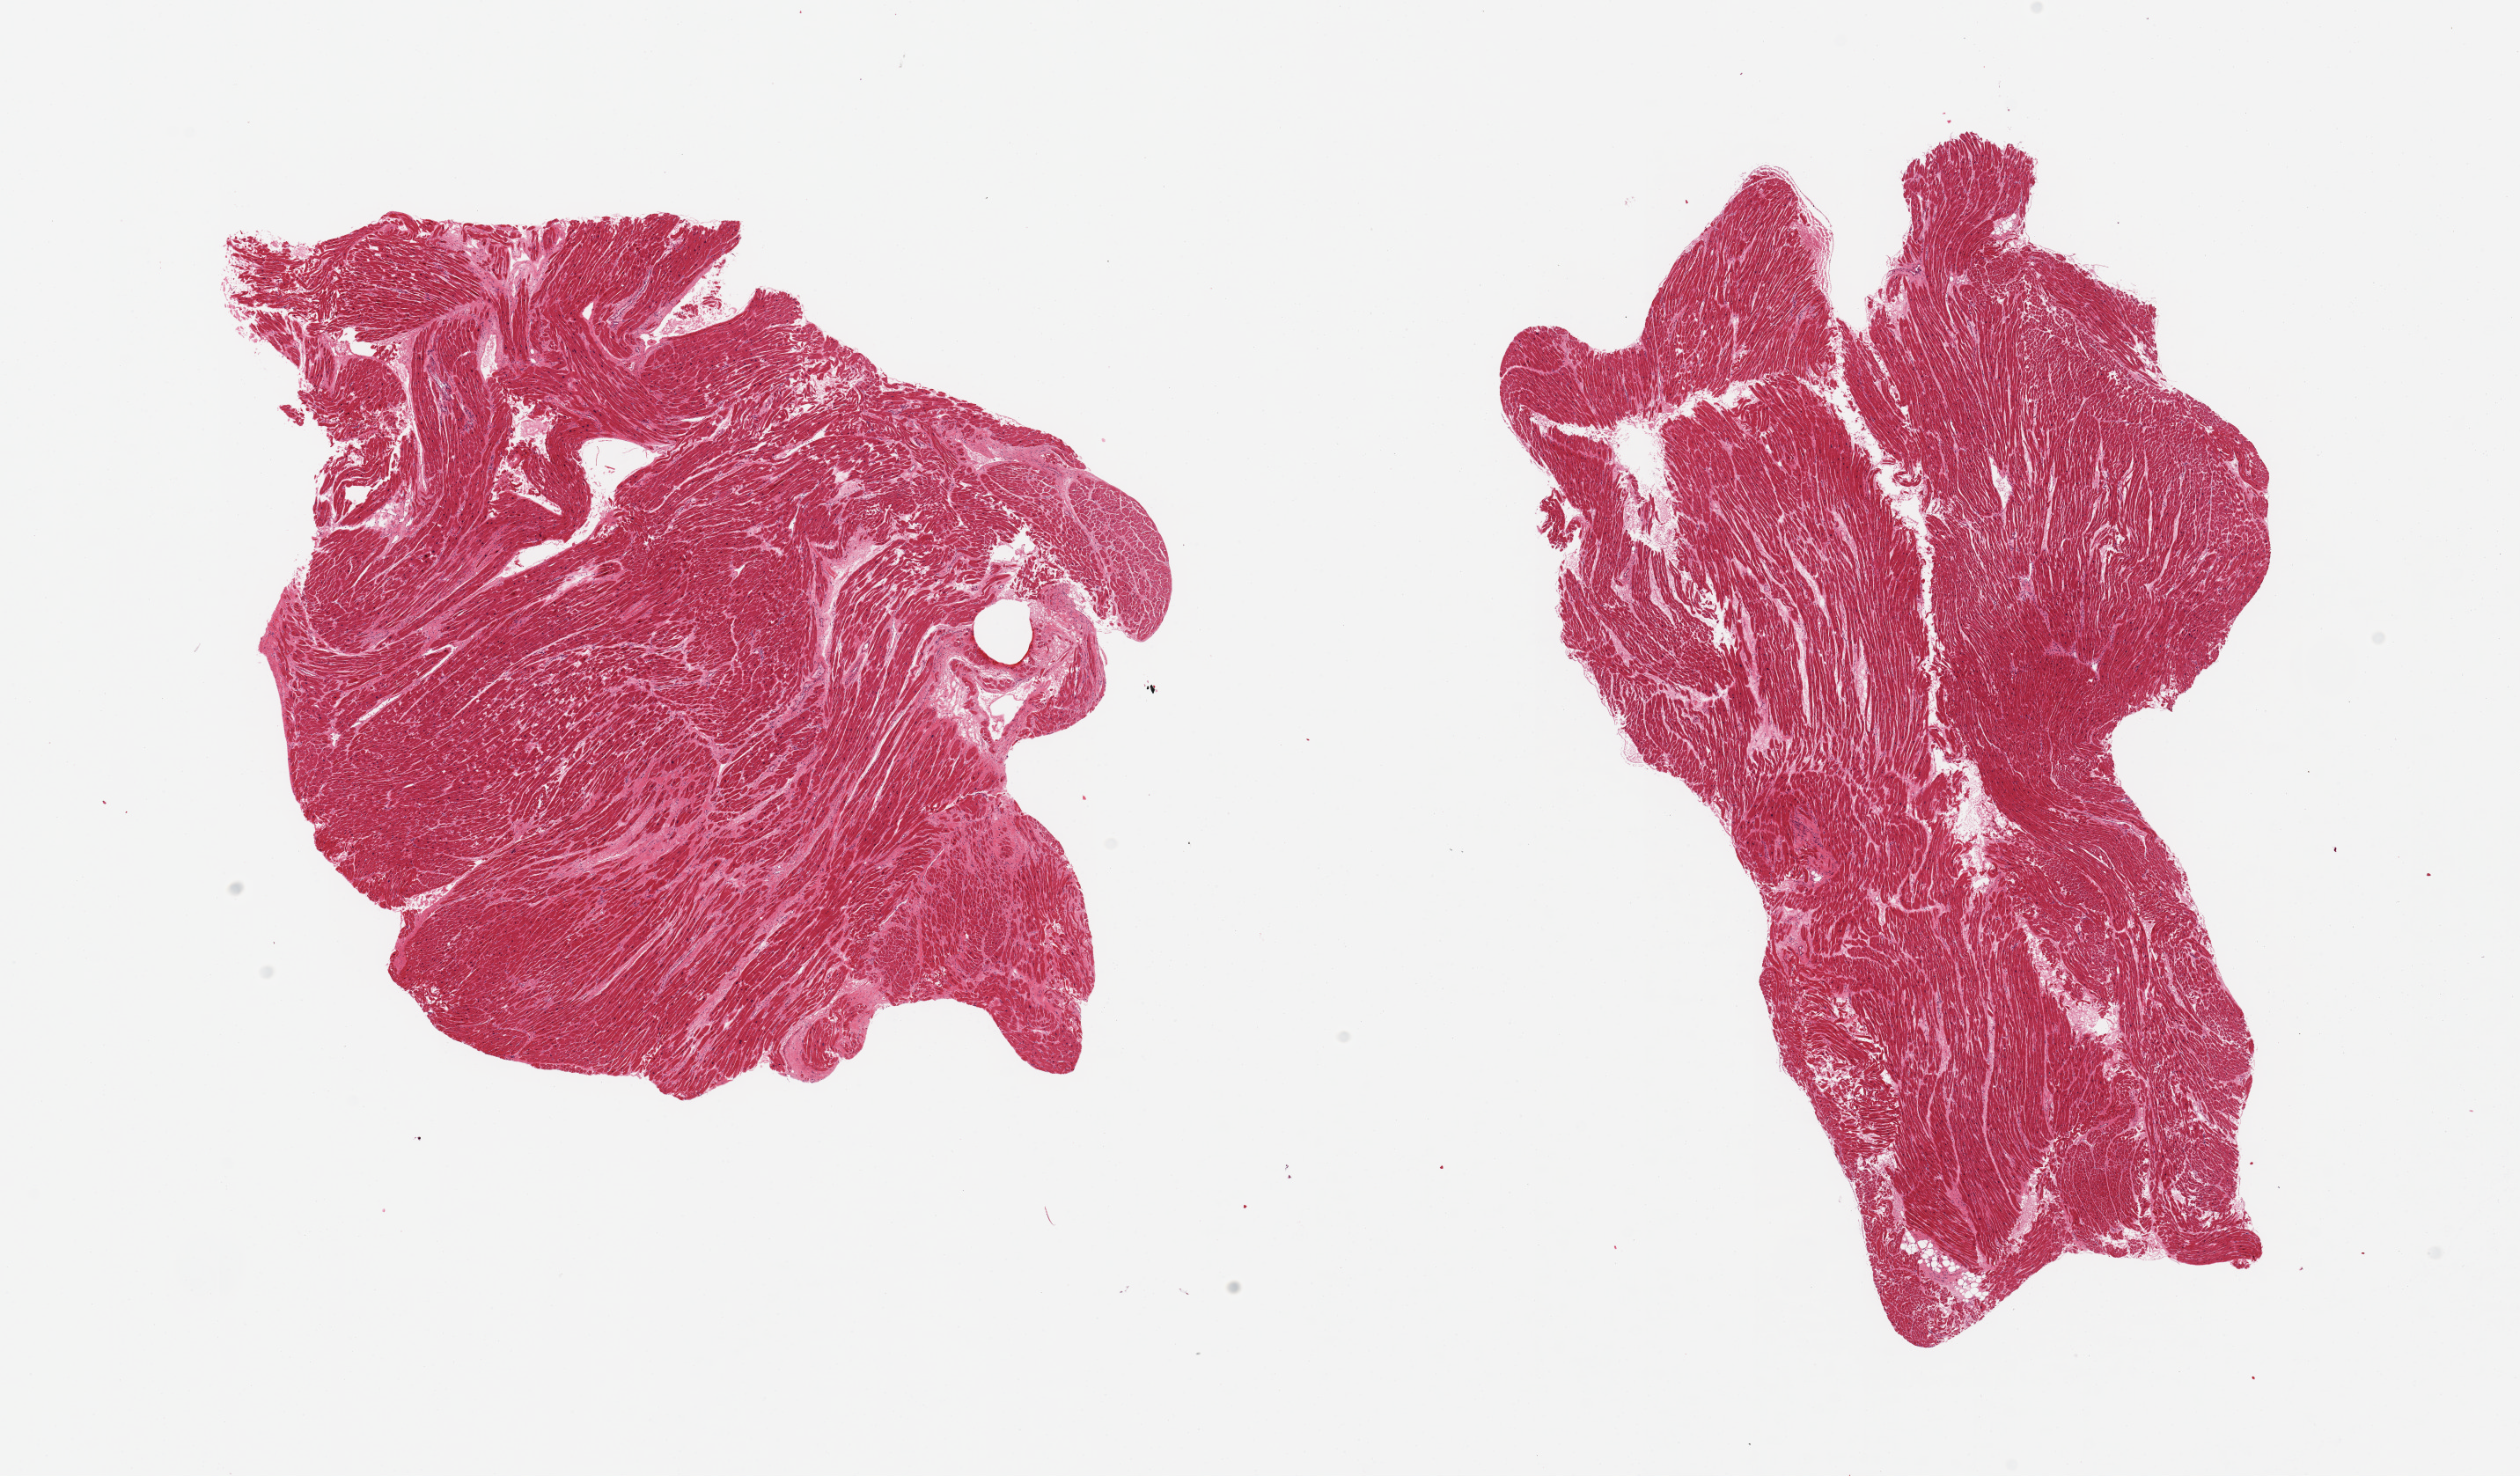
Haematoxylin and eosin whole-slide image, low-resolution overview of the scanned area, about 22.6 x 13.3 mm (acquisition: 20x scan). PAXgene-fixed, paraffin-embedded tissue. Sampled site (target tissue): heart. Tissue donor sample. Donor sex: female.
Pathologist's review note for this sample: 2 pieces; patchy fibrosis.